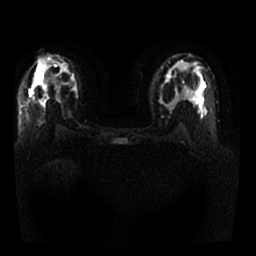
Breast MRI, one axial slice. Slice 15 of 25 in the series (ordered by position). Diffusion-weighted series; image 2 of 4 stored at this slice position (different b-values; order by instance number). 1.5 T. 256 × 256 image matrix. Female patient.
Outlined on this slice (outlined manually by an expert reader):
- tumour on diffusion-weighted imaging: box from (x=29, y=92) to (x=44, y=105) px